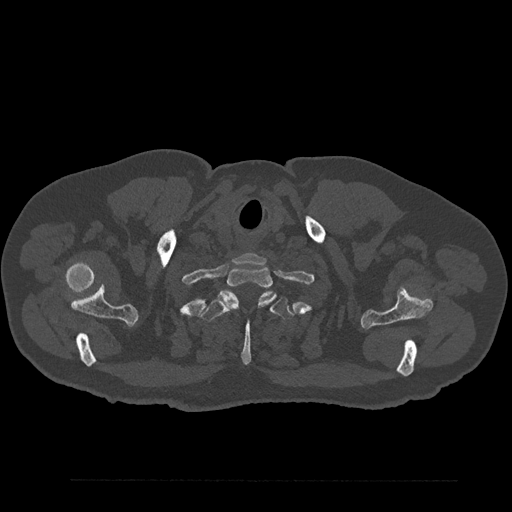
CT including the spine, one axial slice; slice 739 of 797 in the series (ordered by position); reconstruction kernel Br40s/3; bone window (W 1800 / L 400 HU); 0.5 mm slice thickness; 512 × 512 image matrix. Patient: male, 61 years. Case-level facts recorded for this patient, not image findings: primary cancer: prostate.
Structures marked on this image (semi-automatically segmented with operator editing):
- T1 vertebra: bounding box (x1, y1, x2, y2) in pixels: (218, 267, 274, 310)
- T2 vertebra: (200, 291, 295, 365)